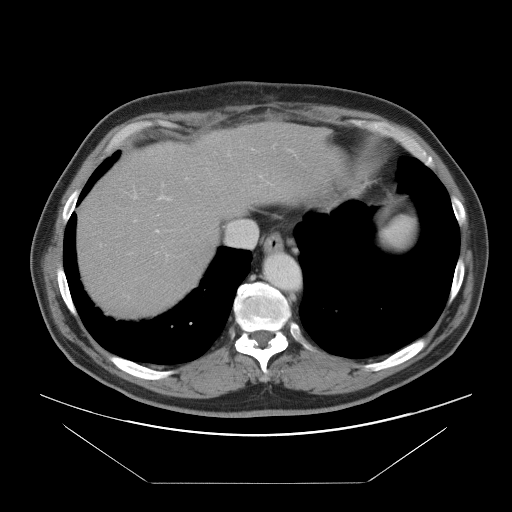
Contrast-enhanced abdominal CT, one axial slice. Slice 79 of 97 in the series (ordered by position). 120 kVp. Intravenous contrast given. Soft-tissue window (W 400 / L 40 HU). 512 × 512 image matrix, field of view 442 × 442 mm. Male patient, age 62 years. Case-level facts recorded for this patient, not image findings: diagnosis: colorectal cancer liver metastases, imaged before liver resection; multiple liver metastases: no; largest metastasis: 7 cm; disease in both lobes: yes.
Outlined on this slice (manually delineated by an expert):
- hepatic veins: bounding box (x1, y1, x2, y2) in pixels: (226, 220, 257, 247)
- liver: (78, 125, 336, 315)
- planned liver remnant (the part of the liver to remain after resection): (77, 174, 222, 315)
- portal vein (with intrahepatic branches): (134, 150, 292, 256)